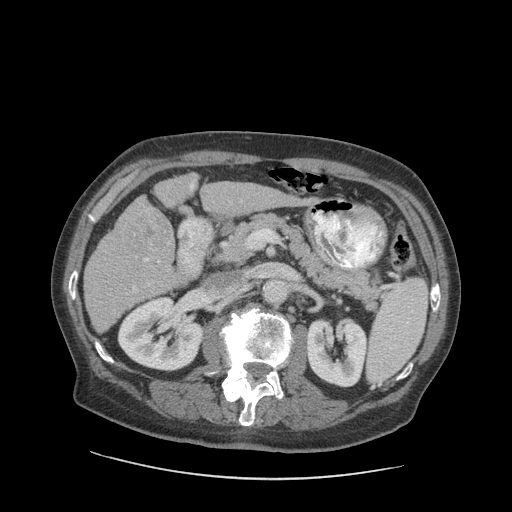
Contrast-enhanced abdominal CT (liver protocol), one axial slice; slice 41 of 89 in the series (ordered by position); soft-tissue window (W 400 / L 40 HU); 2.5 mm slice thickness; 512 × 512 image matrix. From the clinical record (not read from this slice): diagnosis: hepatocellular carcinoma (patient treated with transarterial chemoembolisation; whether this scan precedes or follows treatment is not stated here); TNM stage (as recorded): Stage-I; Child-Pugh class: A; tumour differentiation: moderately differentiated; tumour nodularity: uninodular.
Annotated regions visible in this slice (semi-automatic segmentation, software-assisted and operator-edited):
- liver parenchyma outside the tumour (the mass and vessels are separate outlines, so this box may not span the whole liver): bounding box [x1, y1, x2, y2] px = [84, 174, 296, 332]
- mass: [123, 207, 171, 269]
- liver vessels: [133, 180, 271, 292]